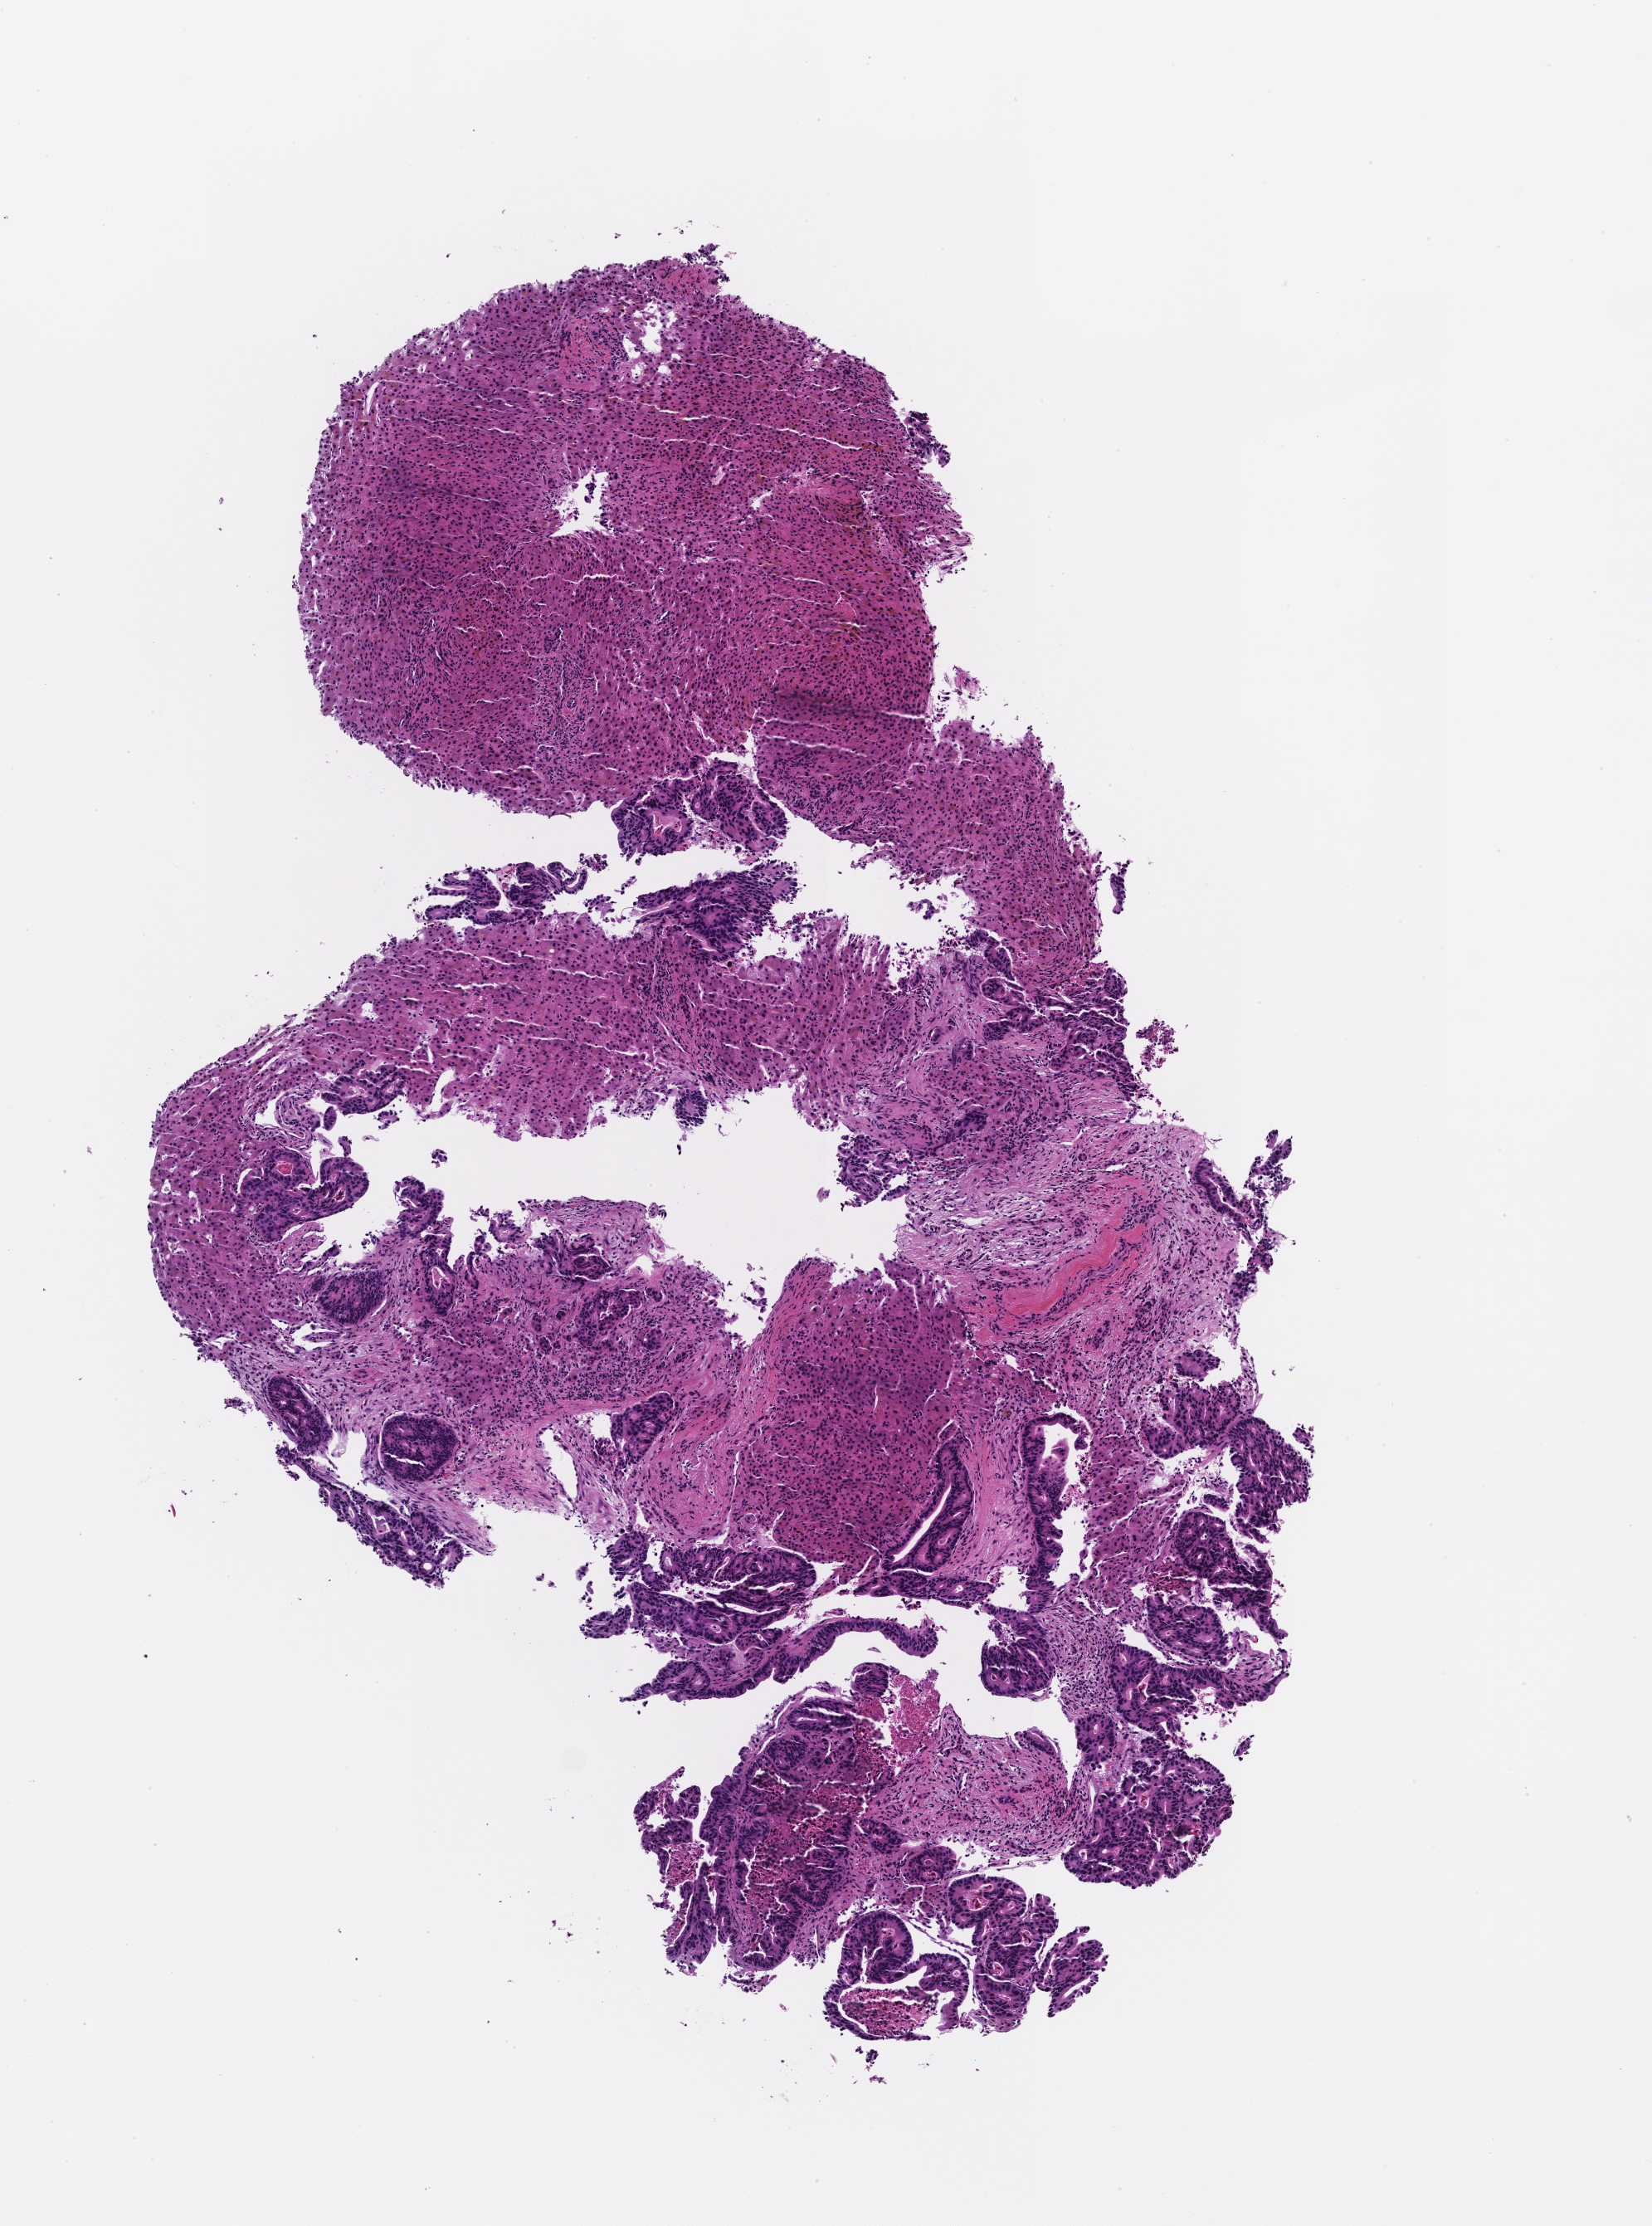
Digitized haematoxylin and eosin-stained section — shown as a low-resolution overview of the whole scanned area (about 4.0 x 5.4 mm); formalin-fixed, paraffin-embedded (FFPE) tissue. Patient: female.
This section: metastasis (sampled organ not recorded). Patient diagnosis (primary): Colorectal Carcinoma.